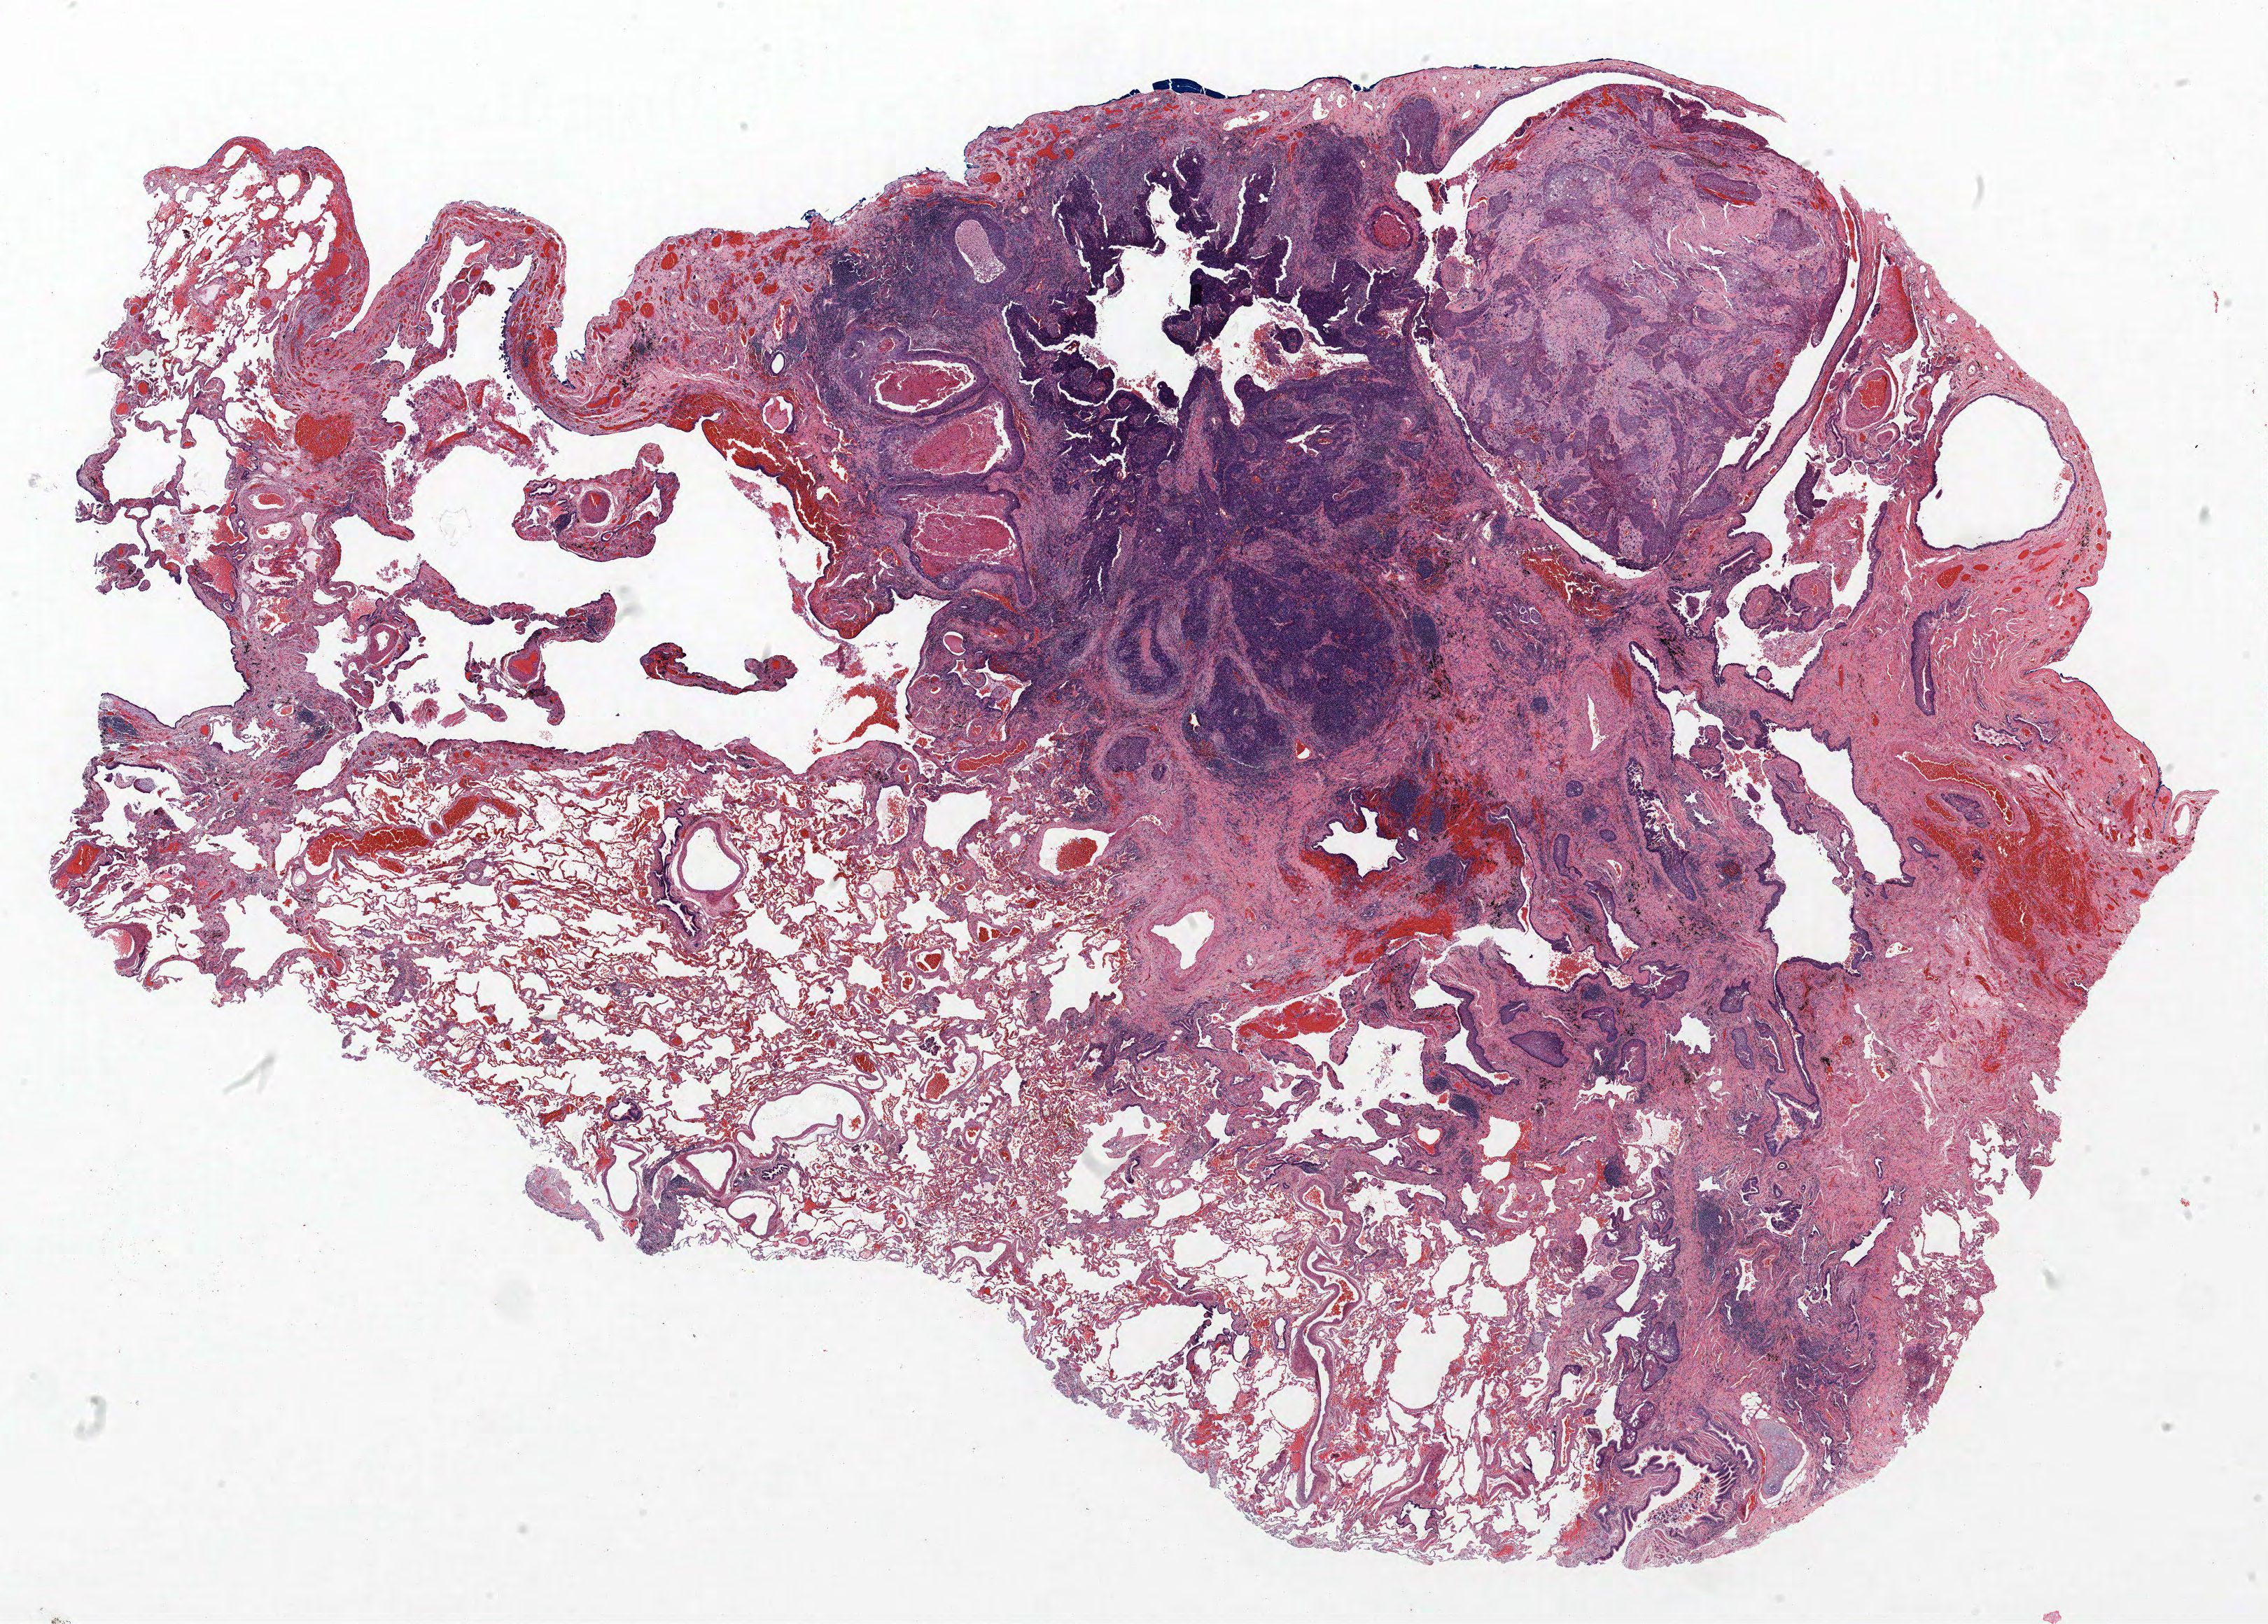
Whole-slide histology image, Hematoxylin and eosin (H&E) stained, a low-resolution overview of the entire scanned area, about 25.9 x 18.6 mm (slide scanned at 40x), FFPE section, lung. Male patient, aged 65 at enrolment. Former smoker at enrolment.
- tumour size (pathology): 20 mm
- participant's lung-cancer diagnosis: Squamous cell carcinoma, NOS (ICD-O-3 8070/3)
- stage (AJCC 6th edition): IB
- primary tumour location (clinical record): left upper lobe
- ICD-O-3 topography: upper lobe of lung (C34.1)